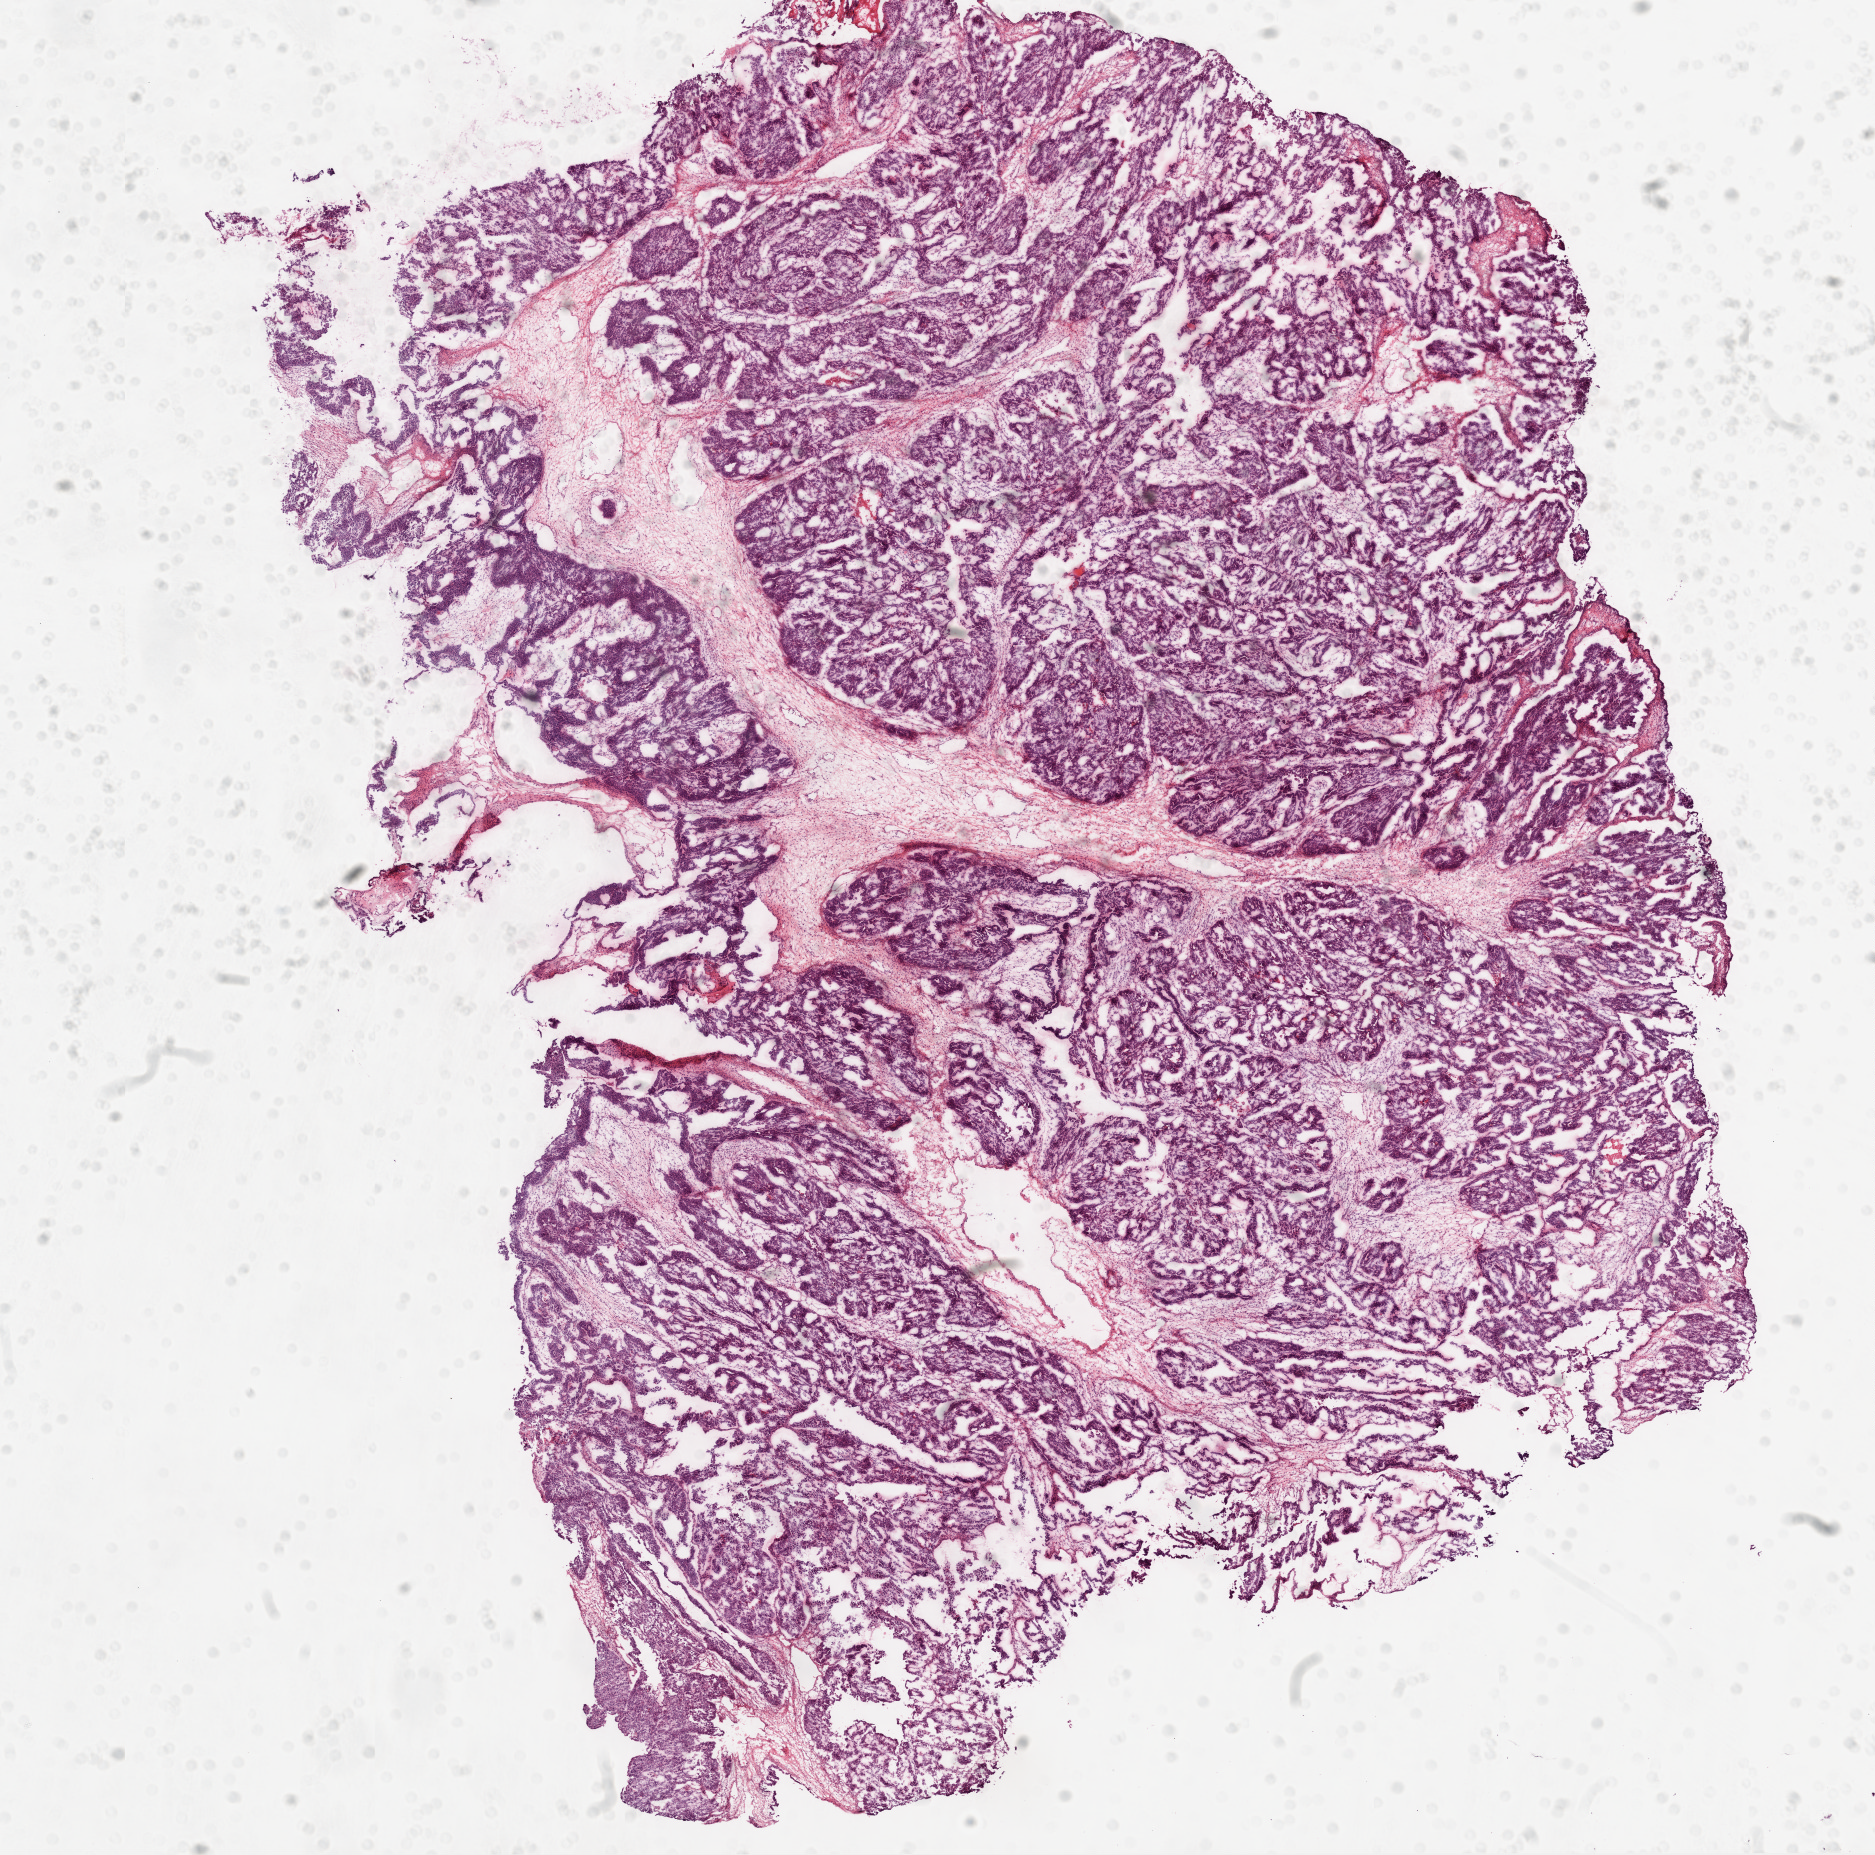
Digitized H&E-stained tissue section (whole slide) — whole scanned area (about 15.0 x 14.9 mm) shown as a low-resolution overview. Frozen section. Ovary, primary tumour sample. Patient: female, age at initial diagnosis 52 years. Histologic grade: G3 (poorly differentiated). Composition of this section per pathologist review: tumour cells 85%, tumour nuclei 95%, normal cells 0%, stromal cells 15%, necrosis 0%.
* FIGO stage: IIIC
* pathologic diagnosis: Serous cystadenocarcinoma, NOS